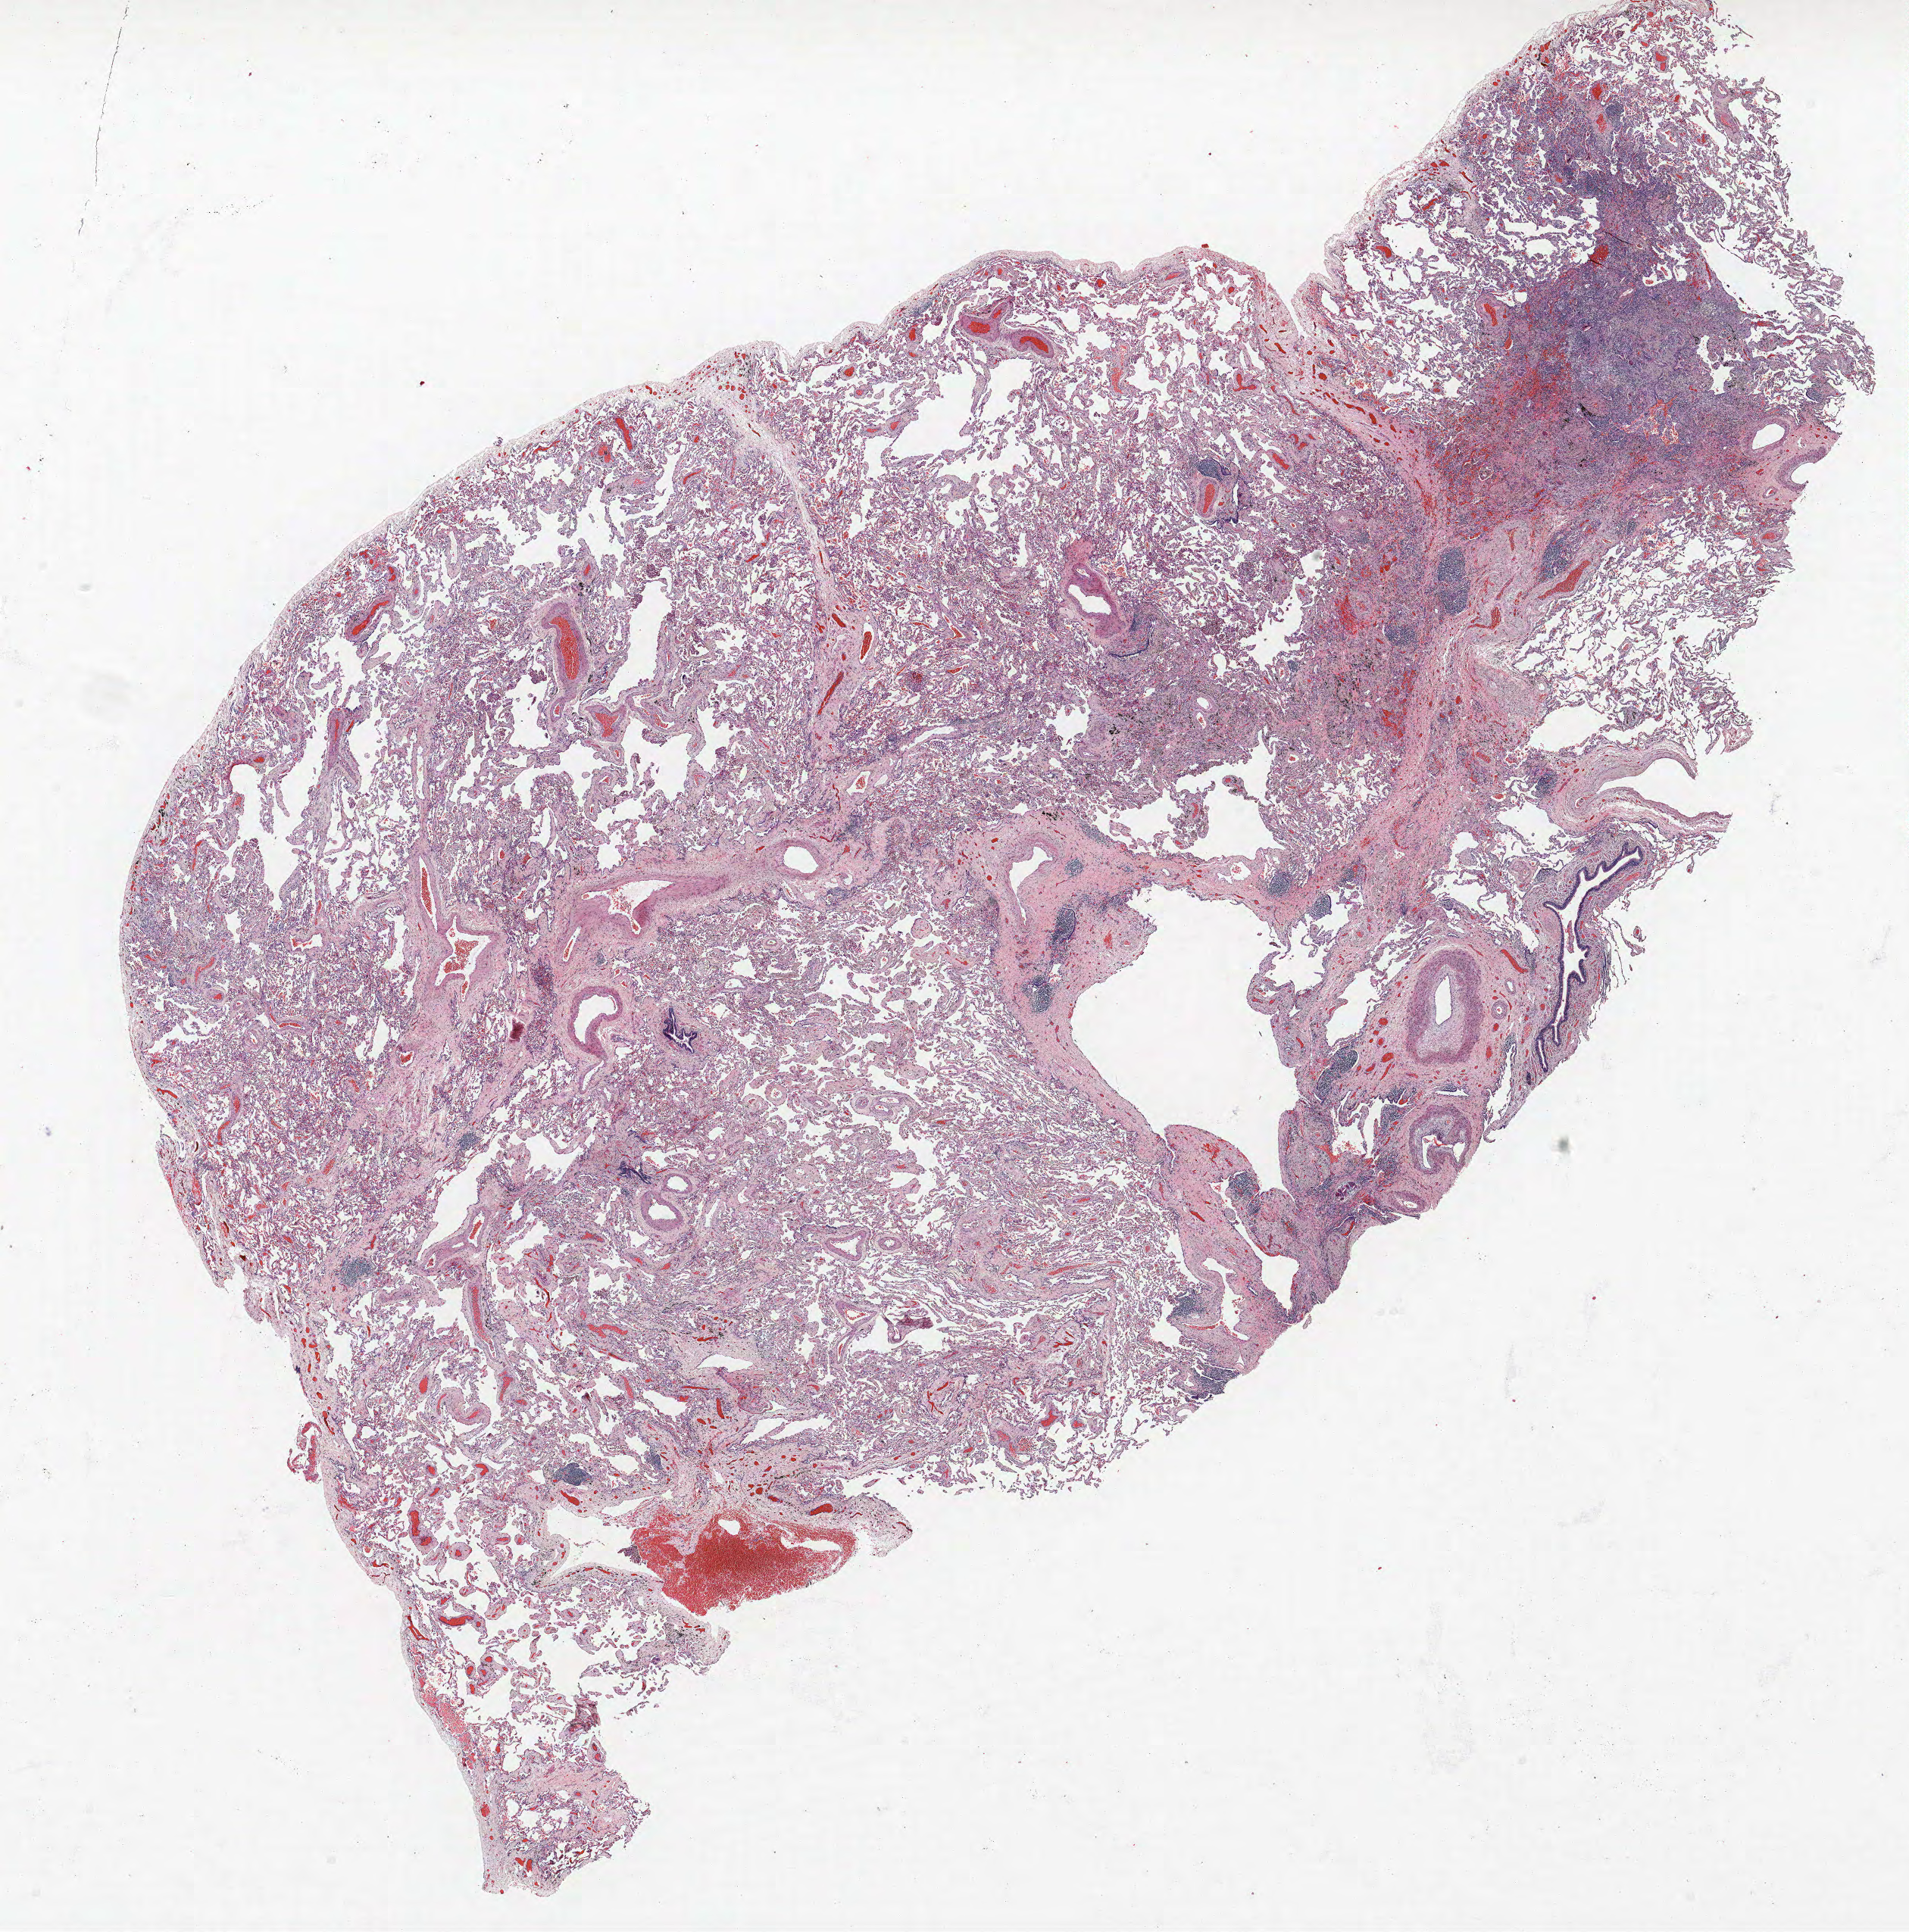
Whole-slide histology image, Hematoxylin and eosin (H&E) stained, low-resolution overview of the scanned area, about 20.2 x 20.4 mm. Formalin-fixed paraffin-embedded (FFPE) section. Lung tissue. Female, age 59 at enrolment. Current smoker at enrolment. Grade: moderately differentiated (G2).
Tumour size (pathology): 28 mm. Participant's lung-cancer diagnosis: Squamous cell carcinoma, NOS. Stage (AJCC 6th edition): IA. Primary tumour location (clinical record): right upper lobe.